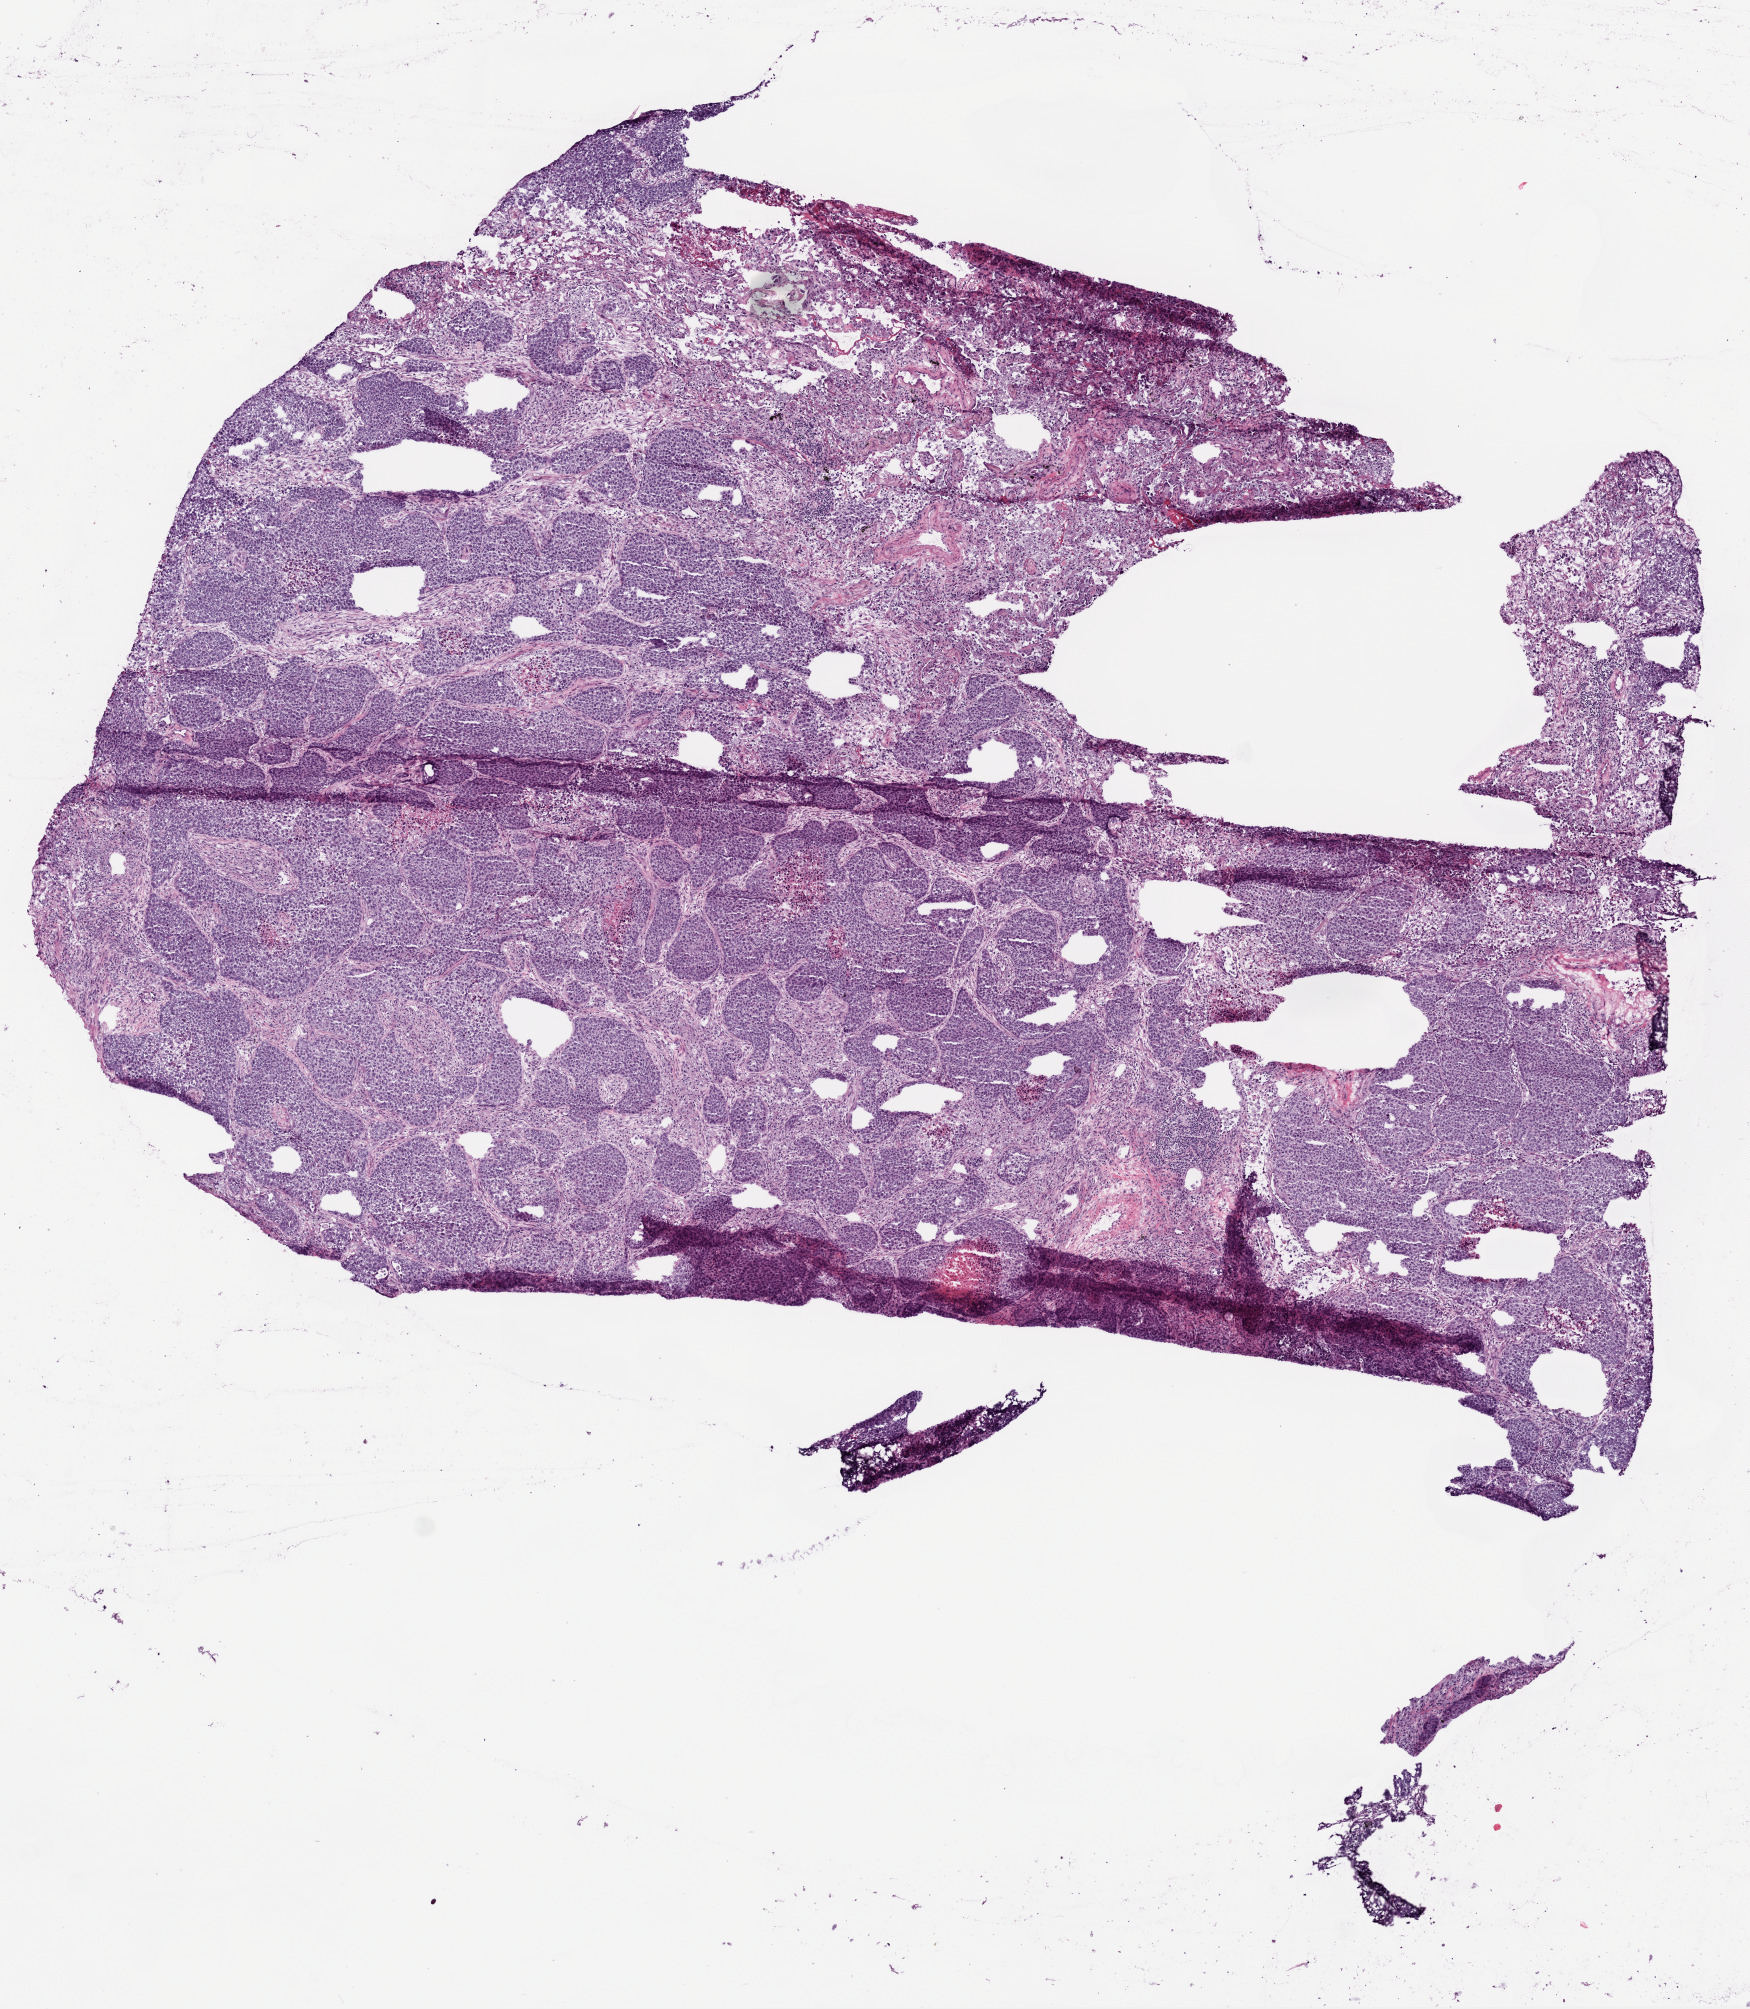
Digitized Hematoxylin and eosin (H&E) stained tissue section (whole slide), whole scanned area (about 7.0 x 8.1 mm) shown as a low-resolution overview. Frozen section from the bottom of the tissue portion. Primary tumour sample from the lung. Male, age 58 years at initial diagnosis. Composition of this section per pathologist review: tumour cells 74%, tumour nuclei 75%, normal cells 8%, stromal cells 10%, necrosis 8%.
AJCC pathologic stage: IIIA. Laterality: left. Diagnosis: Squamous cell carcinoma, NOS (upper lobe, lung).